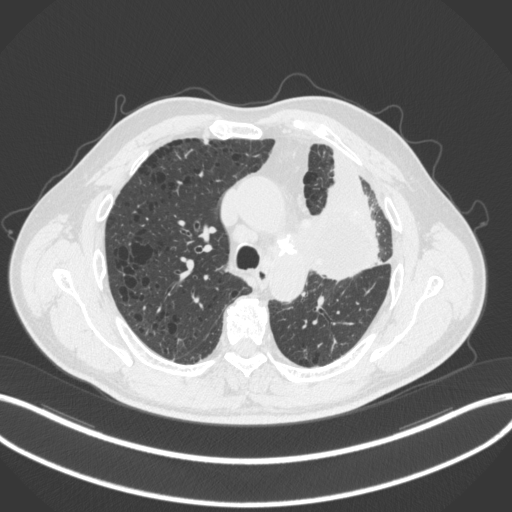
Chest CT, one axial slice; position 202 of 286 along the scan axis; reconstruction kernel B31f; 120 kVp; lung window (W 1500 / L -600 HU); 1 mm slice thickness; 512 × 512 image matrix, field of view 400 × 400 mm. Patient: male, 68 years. From the clinical record (not read from this slice): clinical TNM (as recorded): T3 N3 M1.
Annotated regions visible in this slice (rectangle marked by the reading radiologist):
- lung tumour (recorded histology: adenocarcinoma): box from (x=298, y=175) to (x=387, y=279) px